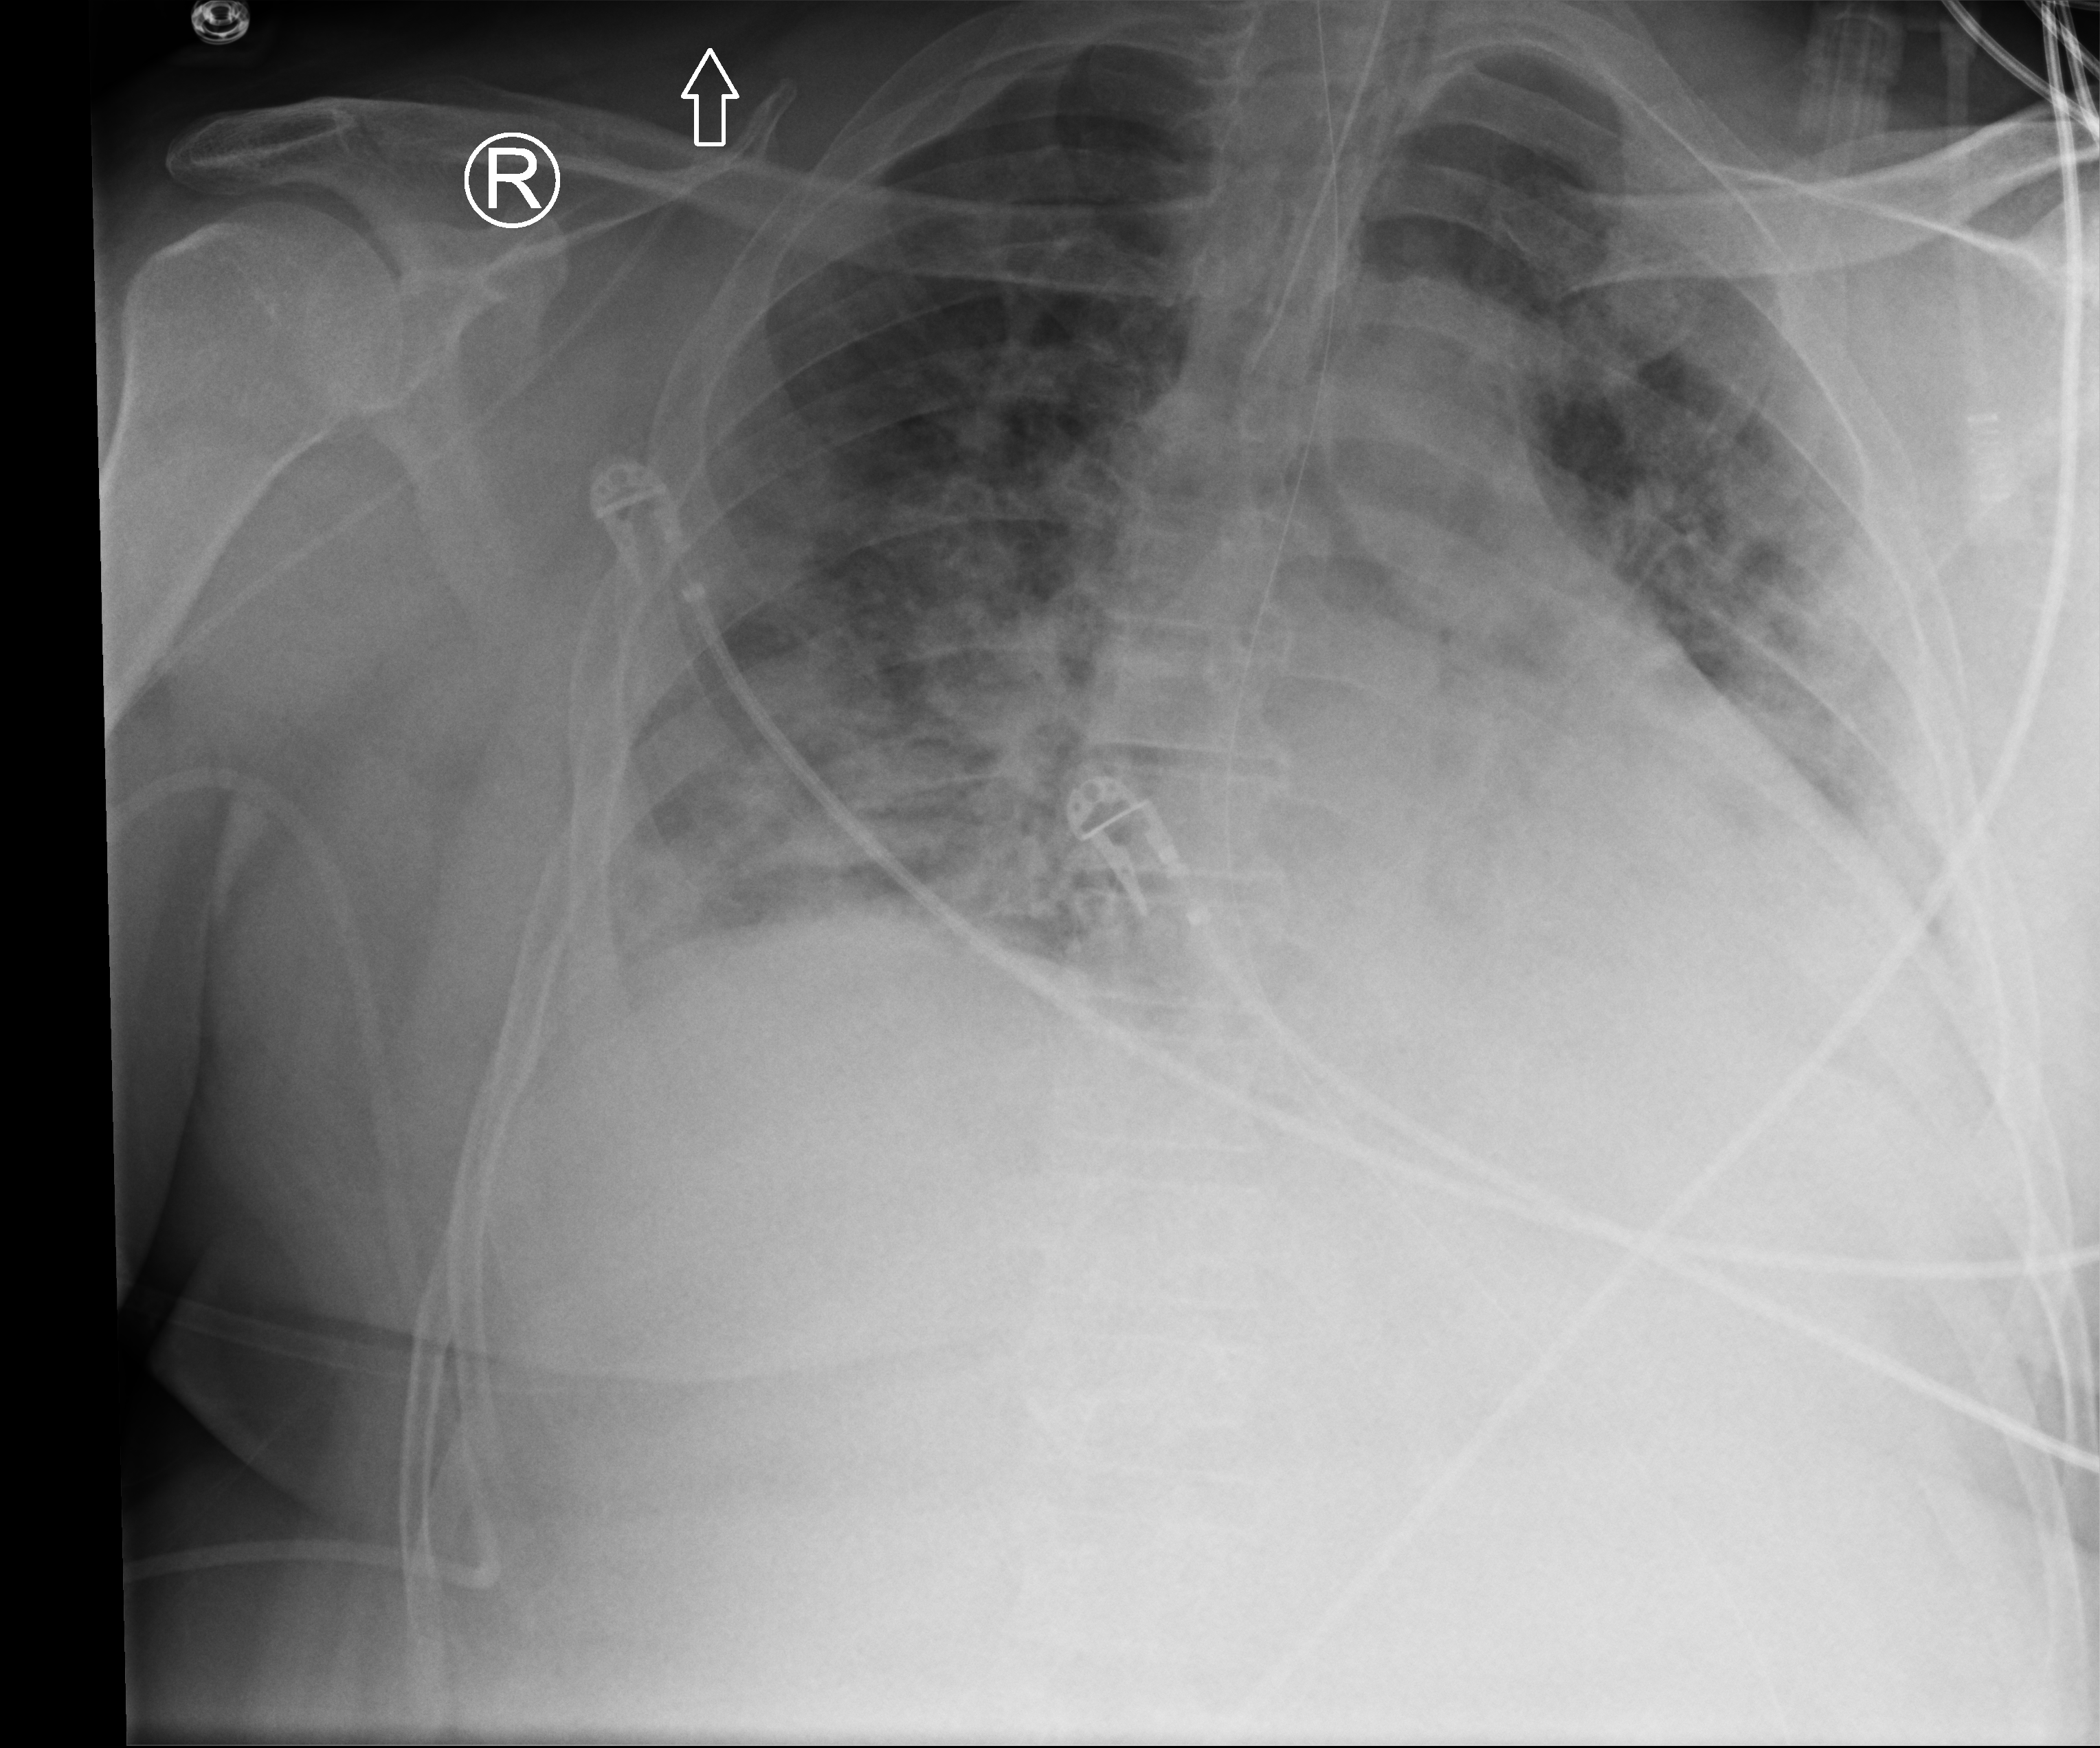
Portable chest radiograph. Male patient hospitalised with COVID-19, age 18–59 years.
Hospital-stay facts (about this admission, not read from this image; timing relative to this image not recorded):
- mechanically ventilated during this hospital stay: yes